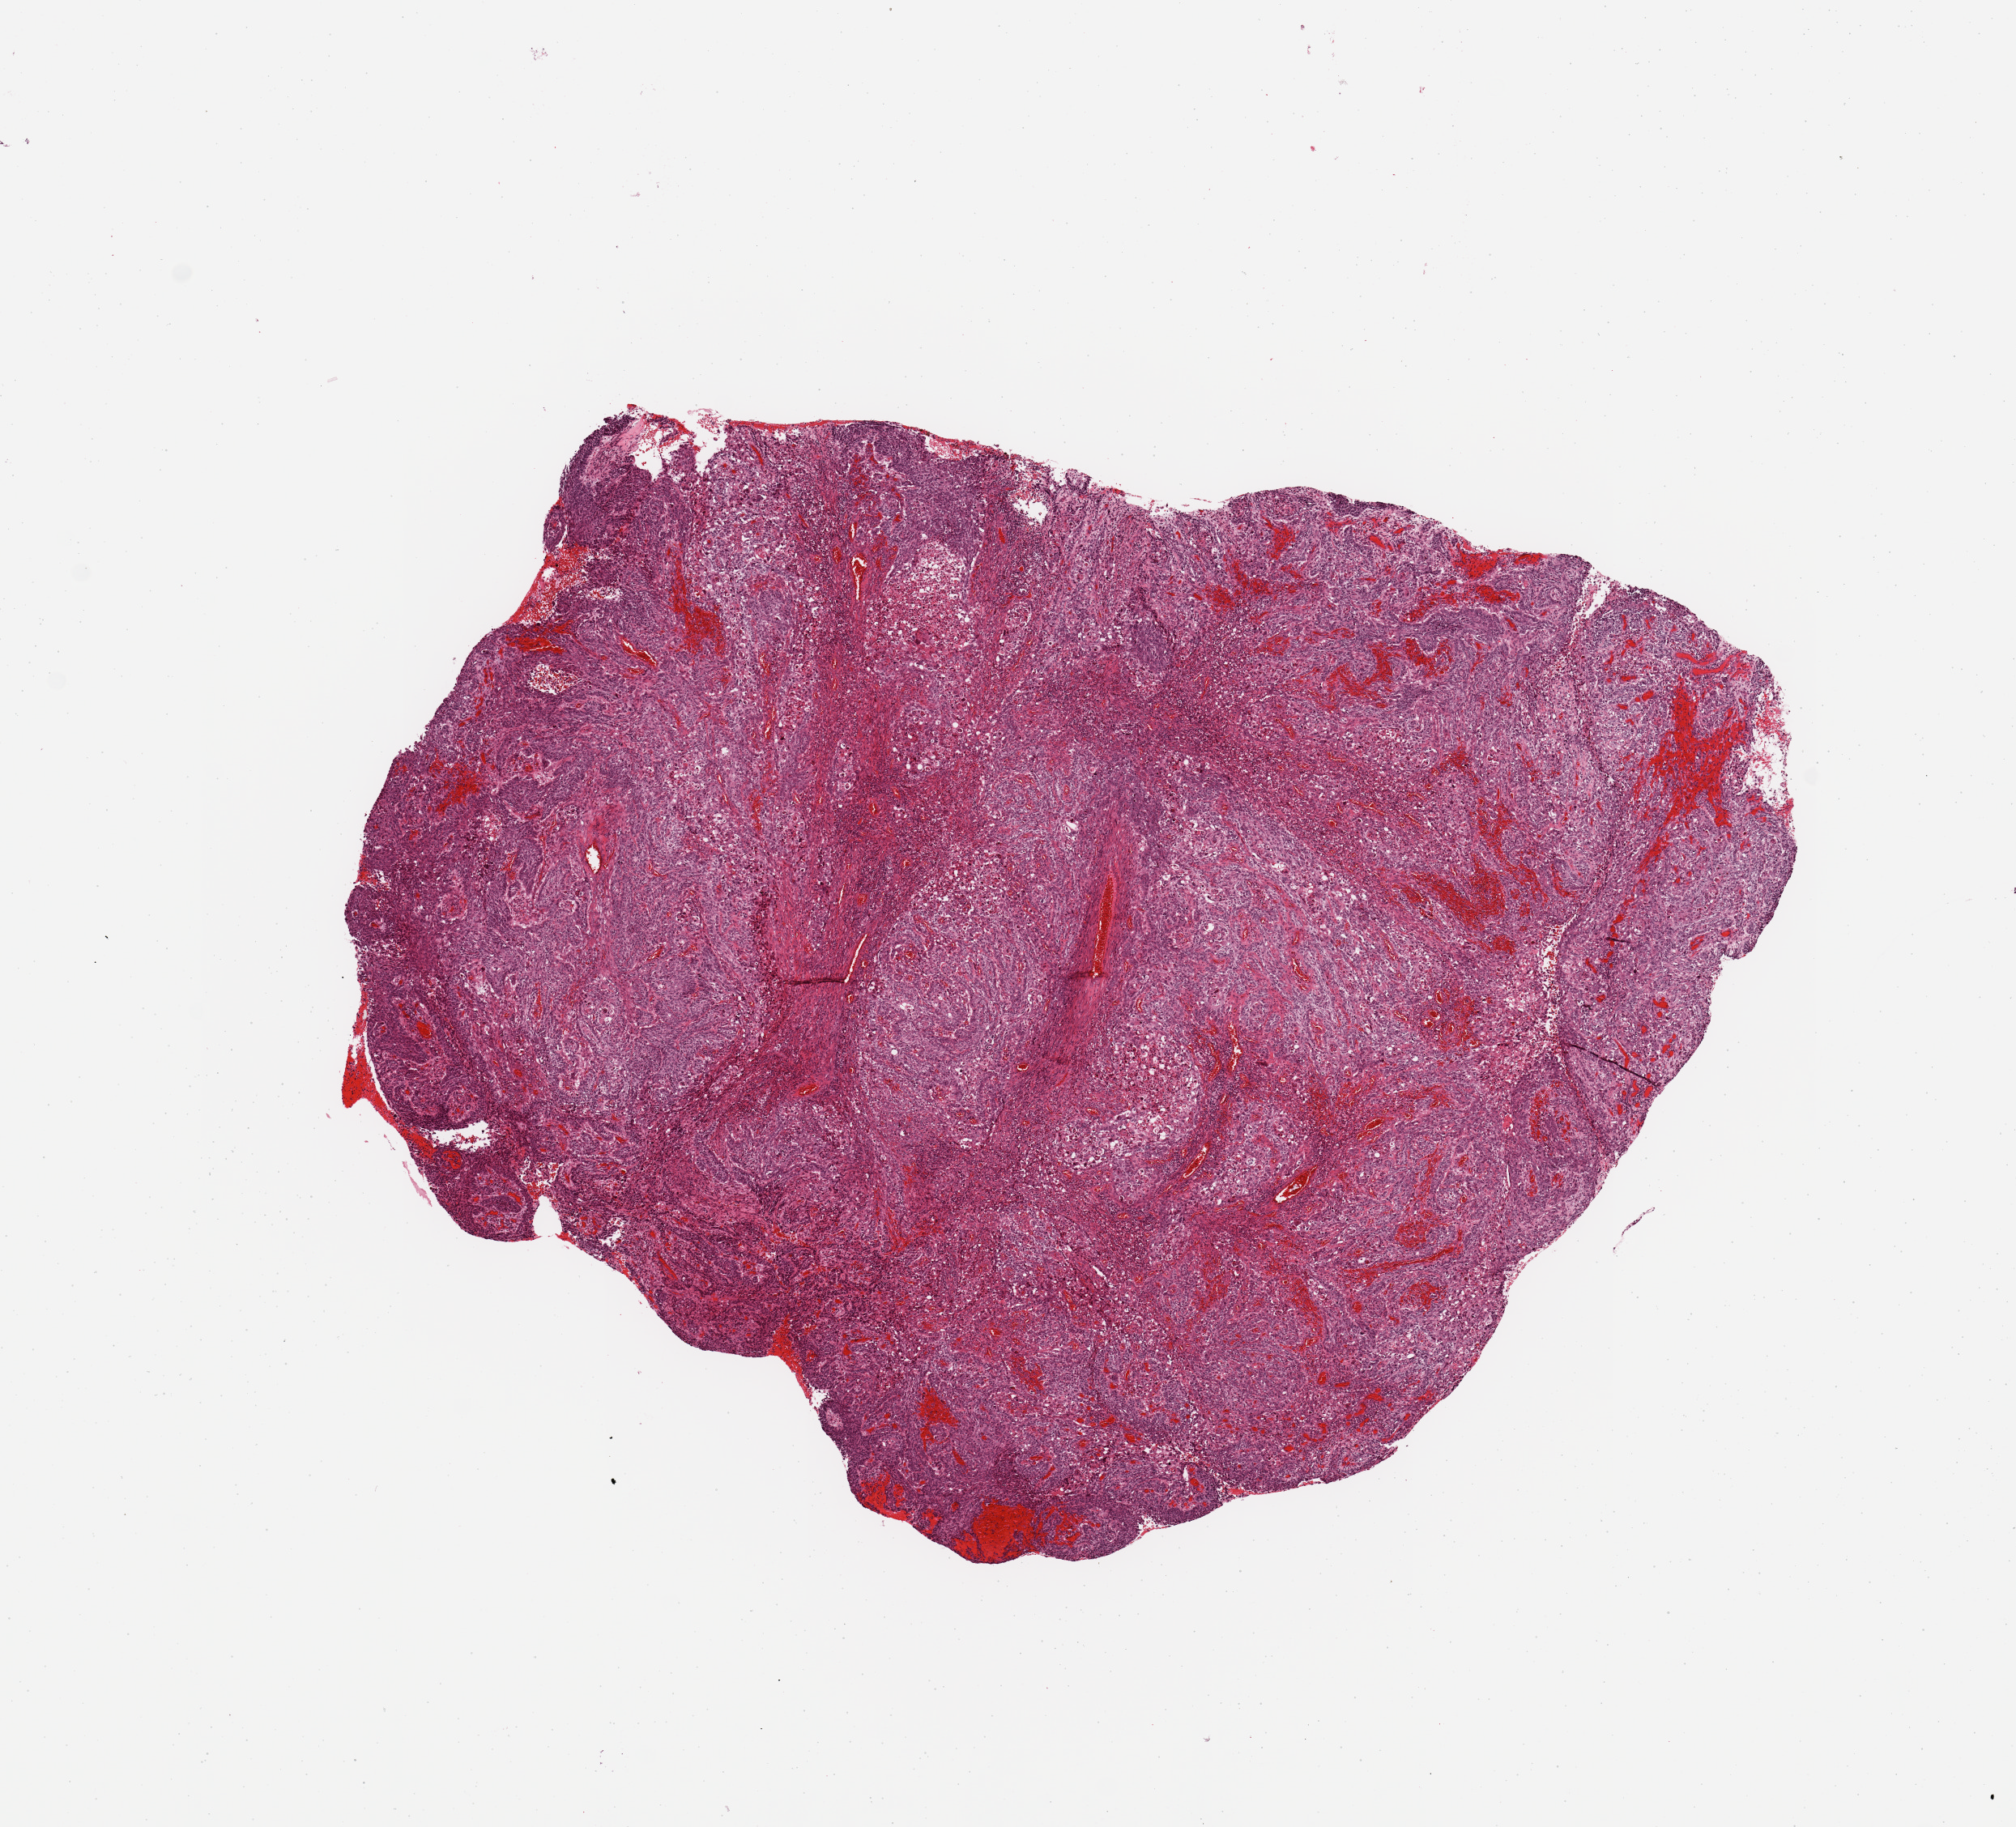
Hematoxylin and eosin (H&E) stained whole-slide image, whole scanned area (about 9.8 x 8.9 mm) shown as a low-resolution overview. Tumour tissue sample, sampled site: lung. Patient: male, age 74 years. Histologic grade: G2 (moderately differentiated). Composition of this section per pathologist review: tumour nuclei 85%, necrosis 0%.
Primary tumour site (as recorded): left lower lobe. Diagnosis: Squamous cell carcinoma, NOS. AJCC pathologic stage: IIIA.